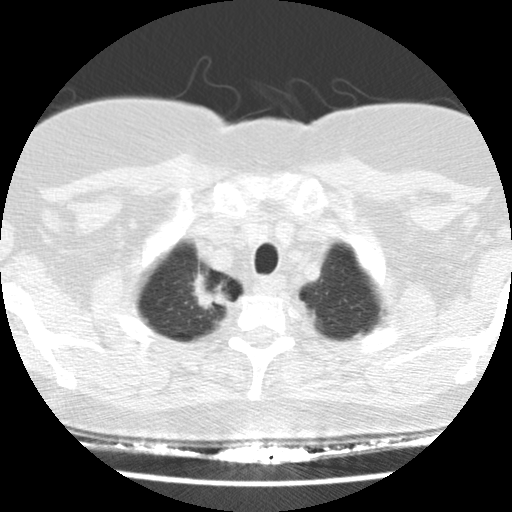
Low-dose screening chest CT, one axial slice; slice 135 of 148 in the series (ordered by position); reconstruction kernel STANDARD; 120 kVp; lung window (W 1500 / L -600 HU); 2.5 mm slice thickness; 512 × 512 image matrix, field of view 281 × 281 mm.
Annotated regions visible in this slice (outlined manually by an expert reader):
- lesion 1 (tumor, upper lobe of right lung): bounding box (x1, y1, x2, y2) in pixels: (193, 273, 233, 310)